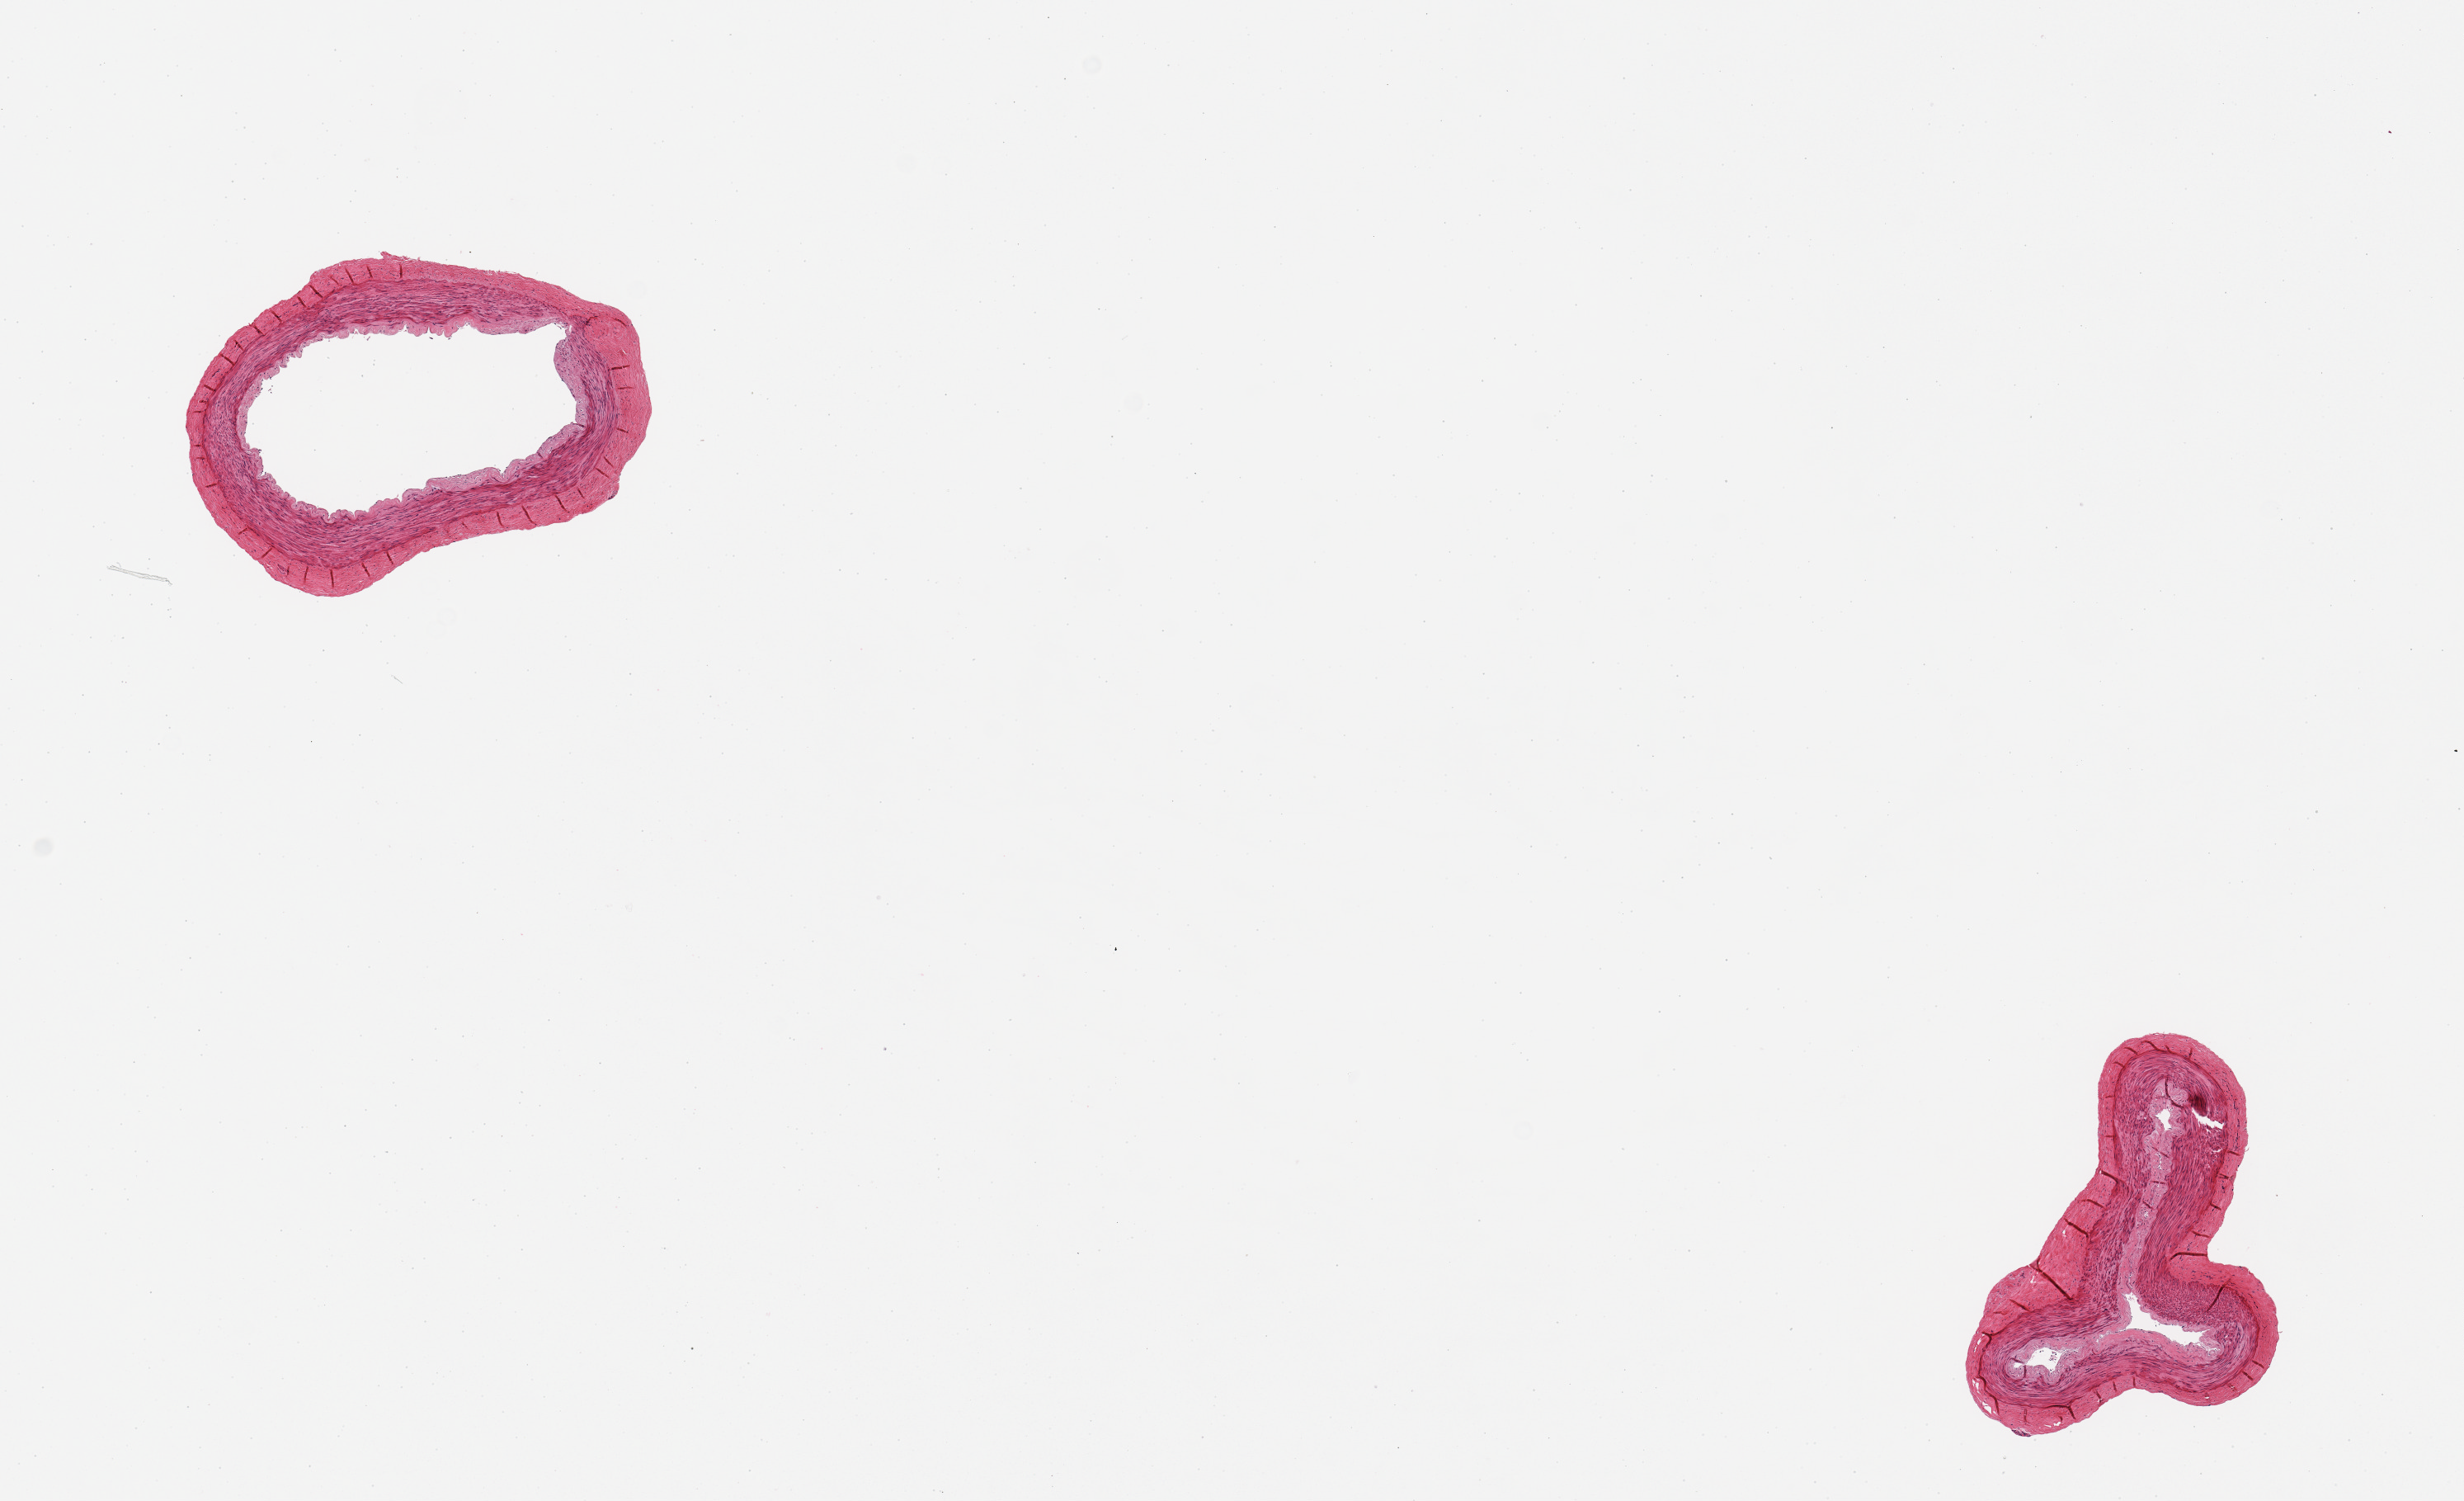
Whole-slide image, haematoxylin and eosin stain, brightfield — whole scanned area (about 11.8 x 7.2 mm, acquisition: 20x scan) shown as a low-resolution overview; PAXgene-fixed paraffin-embedded (PFPE) section; section of tibial artery (target tissue); donor tissue sample. Female donor.
• reviewer comment on this tissue sample: 2 pieces; well trimmed; no leasions